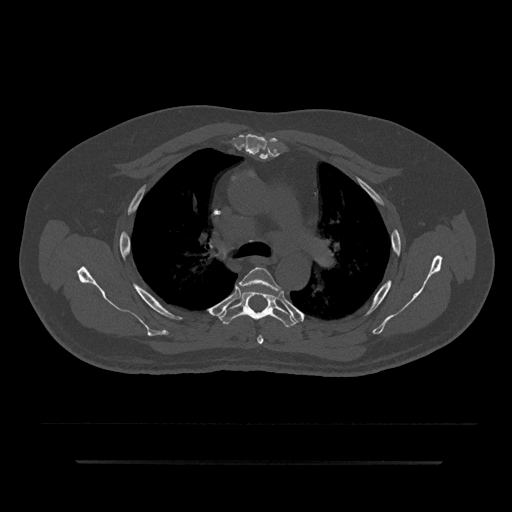
CT including the spine, one axial slice. Slice 590 of 797 in the series (ordered by position). Reconstruction kernel Br40s/3. 120 kVp. Bone window (W 1800 / L 400 HU). 0.5 mm slice thickness. 512 × 512 image matrix, field of view 464 × 464 mm. Patient: male, 59 years. Case-level facts recorded for this patient, not image findings: primary cancer: bile ducts.
Annotated regions visible in this slice (semi-automatic segmentation, software-assisted and operator-edited):
- T4 vertebra: bounding box [x1, y1, x2, y2] px = [239, 267, 281, 345]
- T5 vertebra: [219, 291, 298, 327]